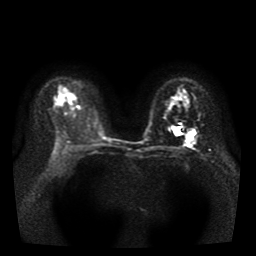
Breast MRI, one axial slice. Position 28 of 43 along the scan axis. Diffusion-weighted series; image 2 of 4 stored at this slice position (different b-values; order by instance number). 1.5 T. 256 × 256 image matrix, field of view 330 × 330 mm. Female patient.
Annotated regions visible in this slice (outlined manually by an expert reader):
- tumour on diffusion-weighted imaging: box from (x=172, y=126) to (x=177, y=136) px